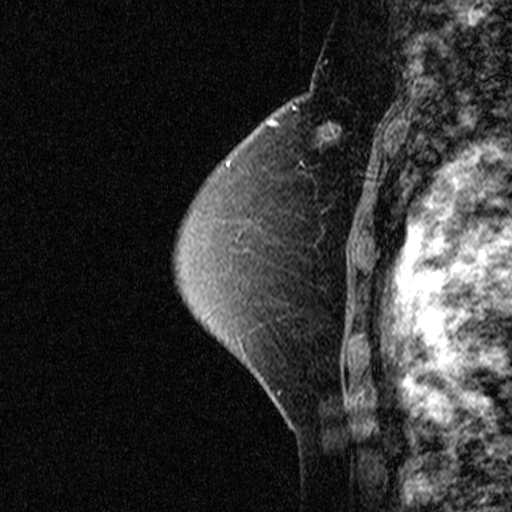
Breast MRI (dynamic contrast-enhanced), one sagittal slice; slice 30 of 44 in the series (ordered by position); dynamic contrast-enhanced study with each time point stored as its own series, time point 2 of 3 at this slice position (early post-contrast, ordered by acquisition time); 1.5 T; TE 4.5 ms, TR 11 ms; 3 mm slice thickness; 512 × 512 image matrix, field of view 200 × 200 mm. Patient: female, 49 years. From the clinical record (not read from this slice): setting: breast cancer imaged before/during neoadjuvant chemotherapy; receptor status: triple-negative.
Structures marked on this image (semi-automatic segmentation, software-assisted and operator-edited):
- analysis volume of interest (the breast-tissue region the enhancement analysis was run in; not a lesion): bounding box [x1, y1, x2, y2] px = [276, 94, 369, 181]
- tumour enhancement mask (voxels above the 90 % enhancement threshold inside the analysis volume of interest): [294, 107, 341, 136]